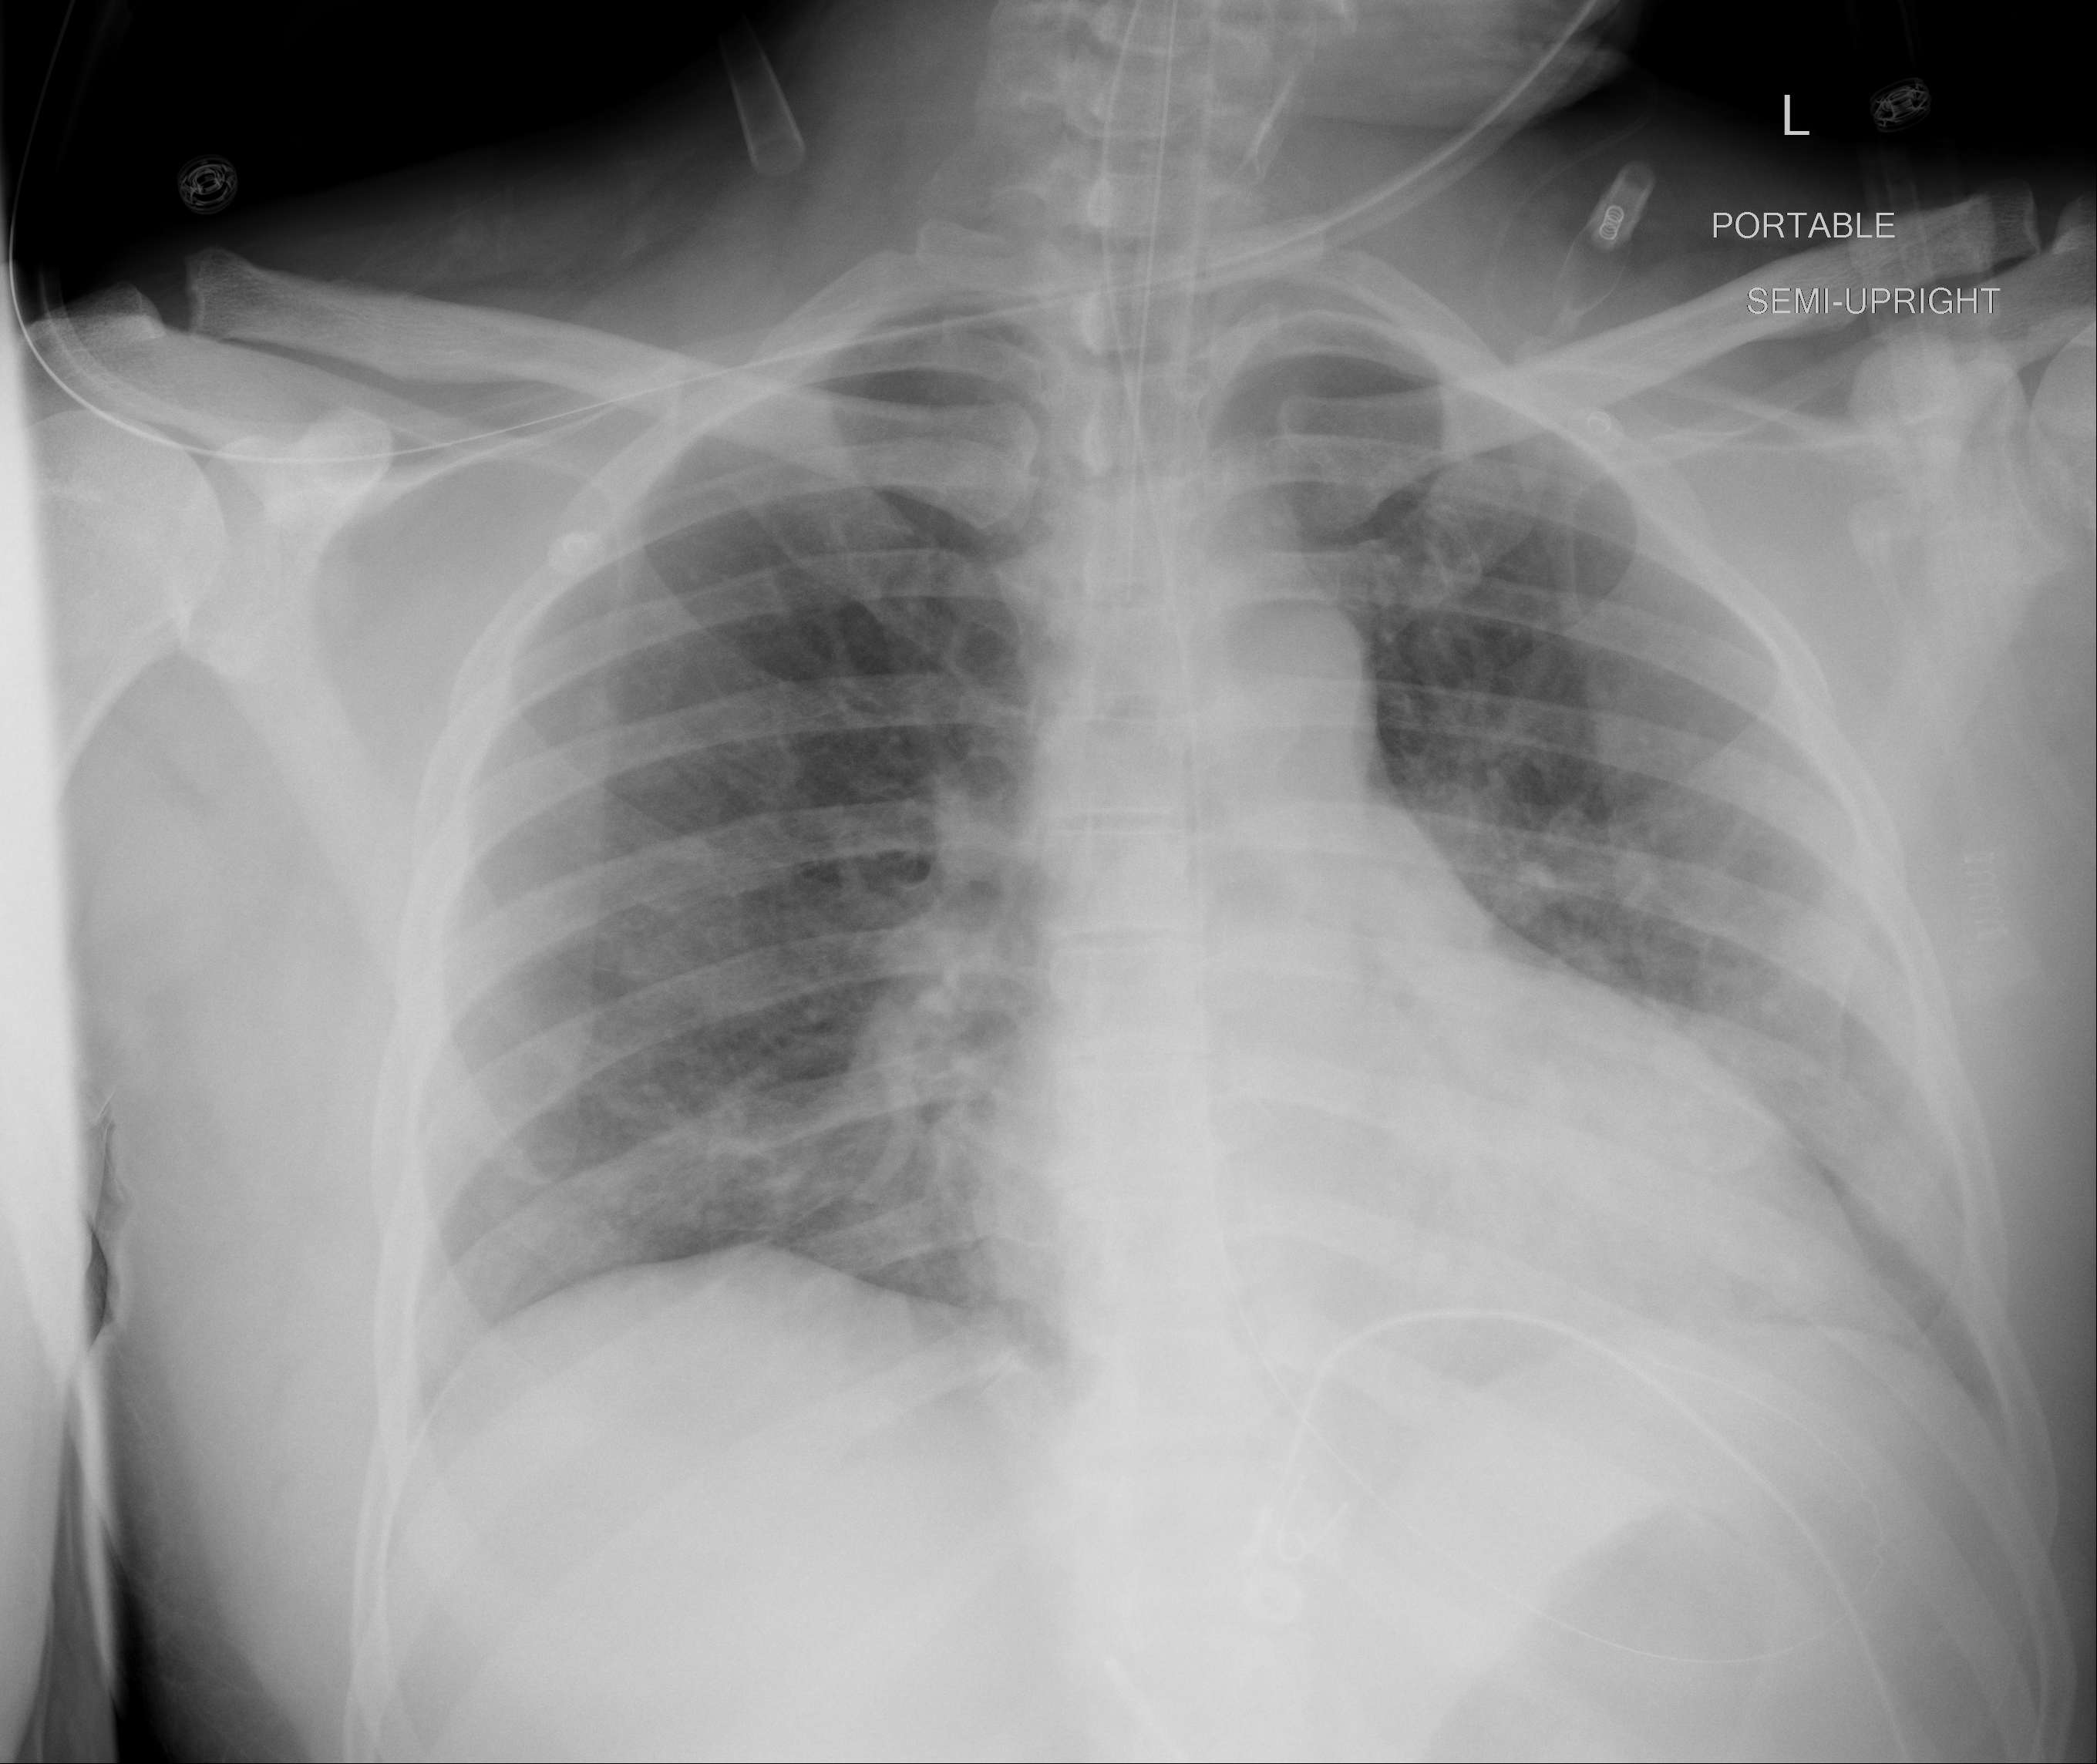
Chest X-ray (portable), AP projection. Male patient, age 44 years; imaged 2 days after the COVID-19 diagnosis.
Radiologist key findings (as recorded): Patchy, airspace opacities are seen within the bilateral lower lungs, predominantly left-sided. Haziness of the left costophrenic angle.